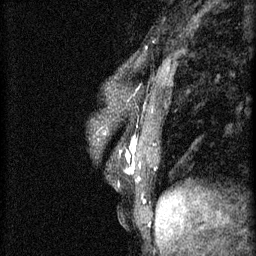
Breast MRI (dynamic contrast-enhanced), one sagittal slice; slice 19 of 60 in the series (ordered by position); 3 images stored at this slice position (order not interpretable as contrast timing); 1.5 T; TE 4.2 ms, TR 11 ms; 256 × 256 image matrix, field of view 180 × 180 mm. Patient: female, 37 years.
Outlined on this slice (semi-automatic segmentation, software-assisted and operator-edited):
- analysis volume of interest (the breast-tissue region the enhancement analysis was run in; not a lesion): bounding box (x1, y1, x2, y2) in pixels: (98, 118, 159, 175)
- tumour enhancement mask (voxels above the 70 % enhancement threshold inside the analysis volume of interest): (126, 136, 137, 175)